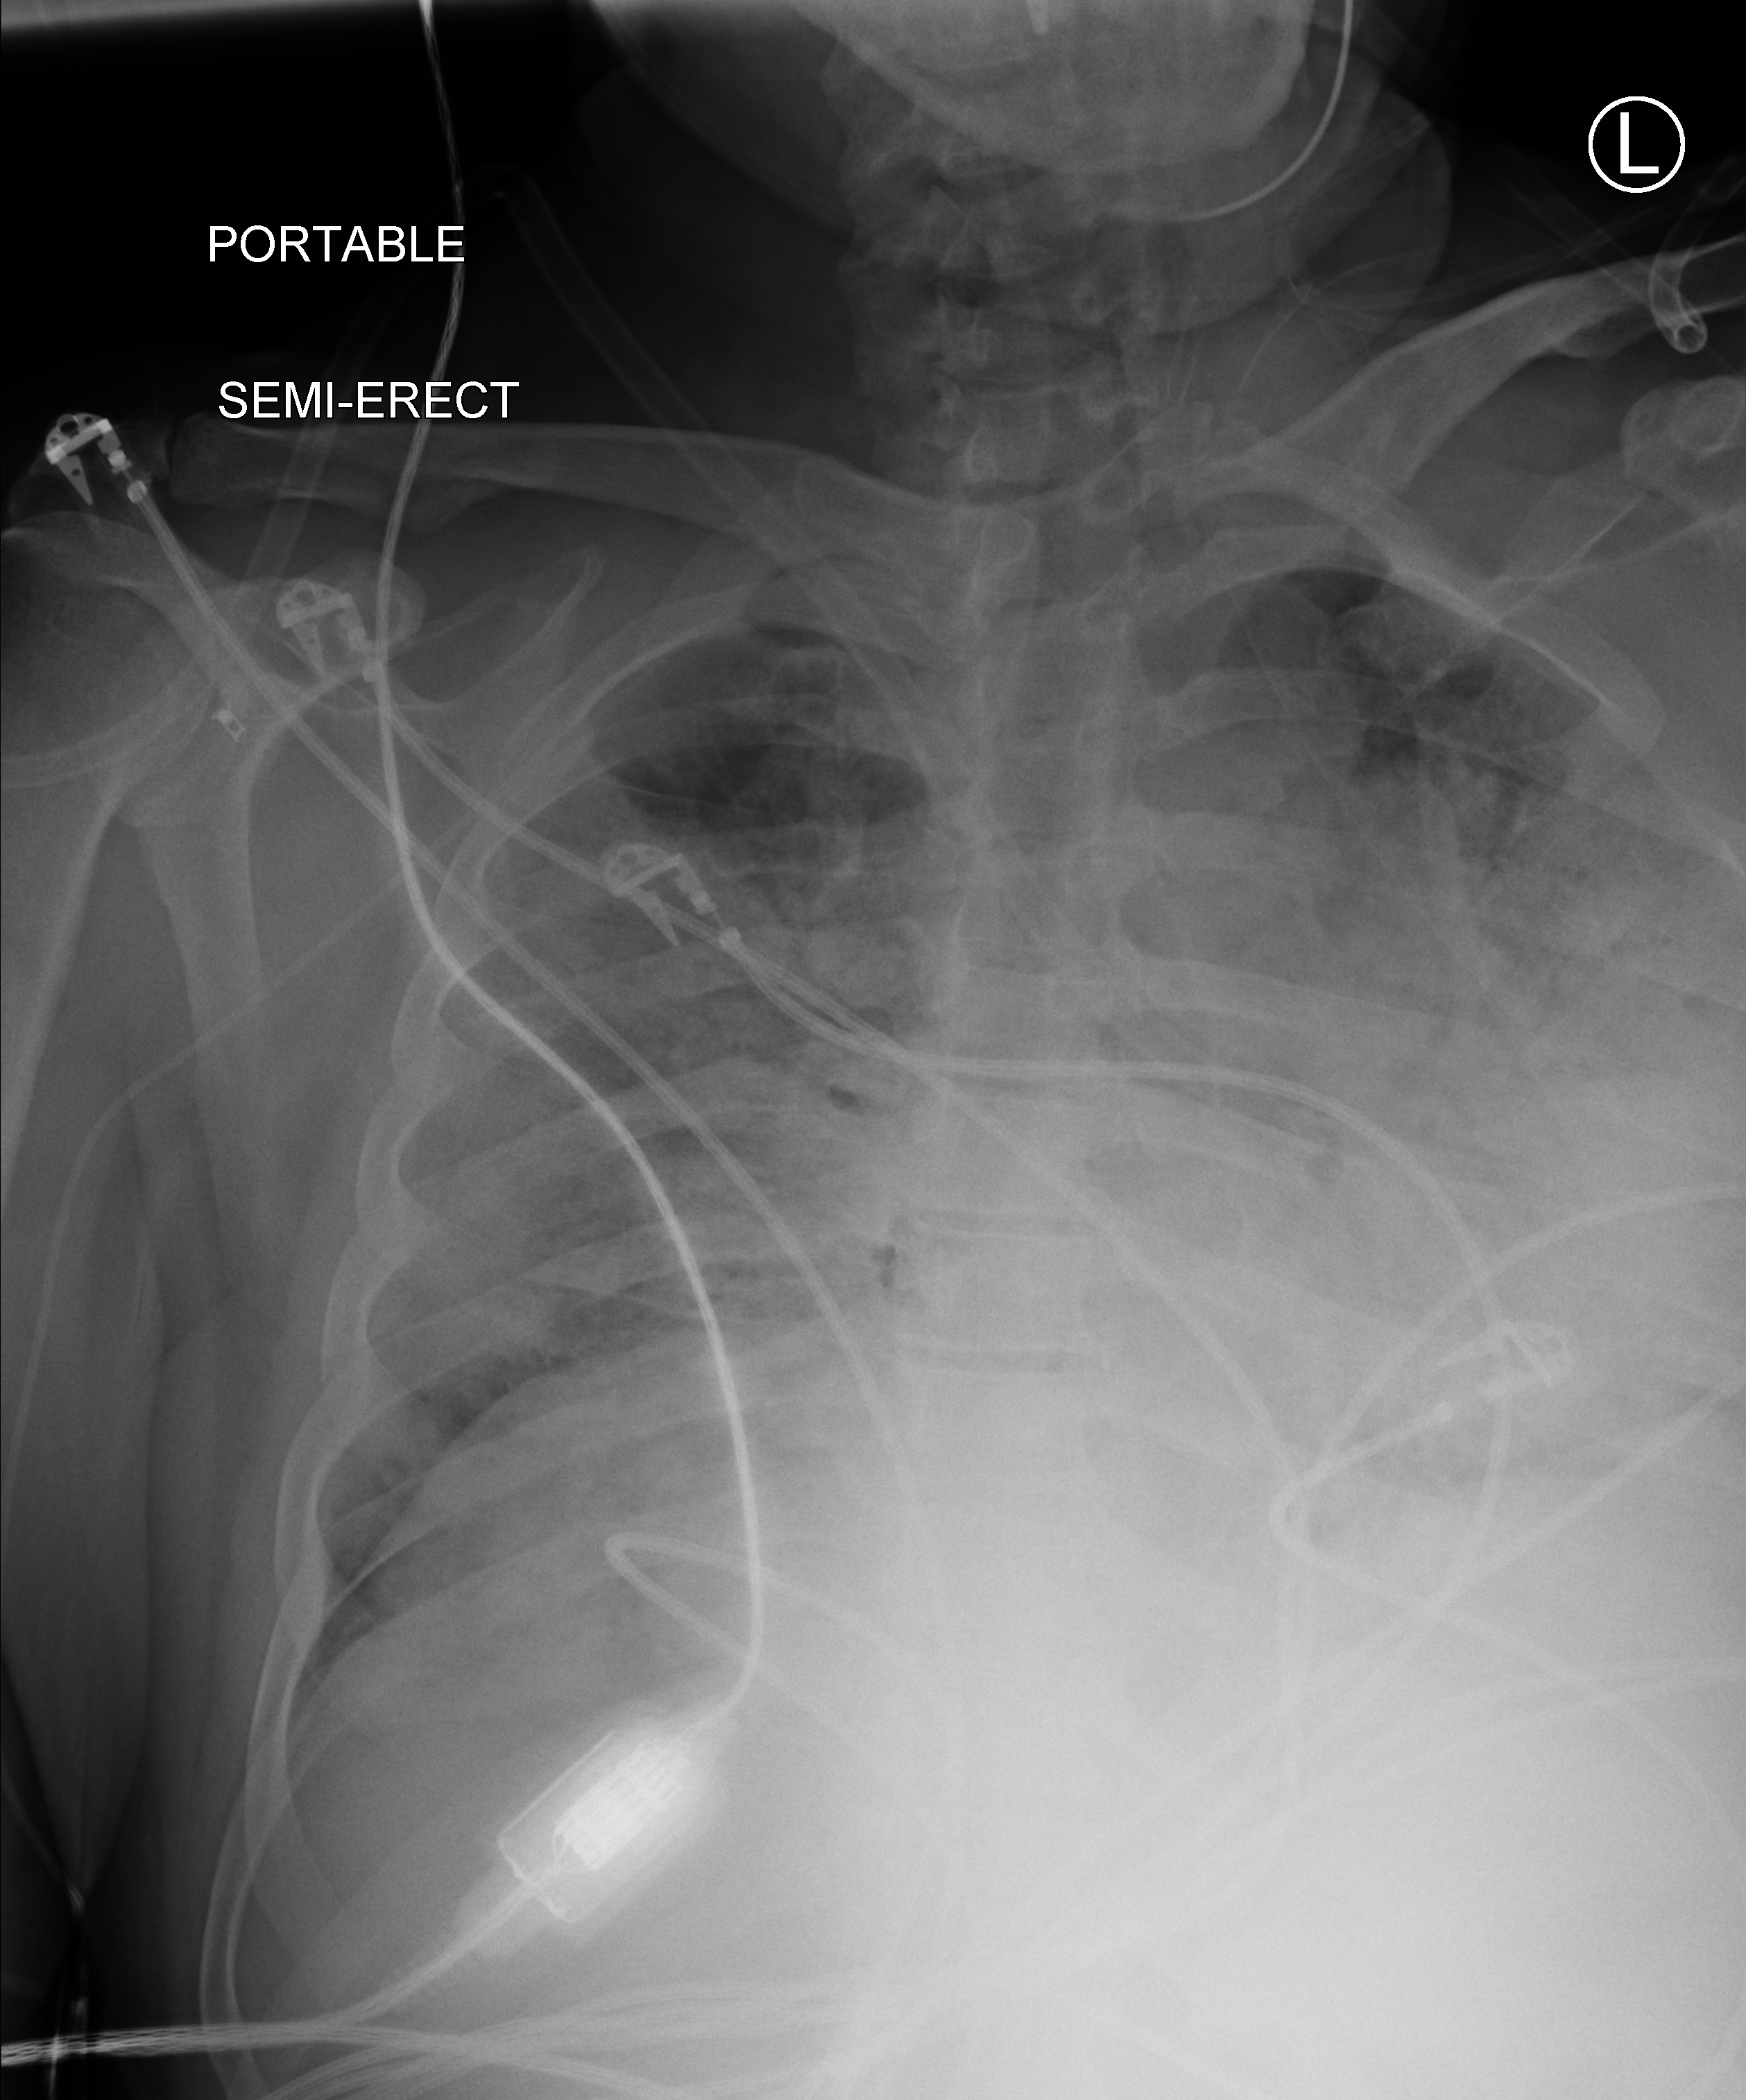
Portable chest radiograph; anteroposterior (AP) projection. Male patient hospitalised with COVID-19, age 18–59 years.
Hospital-stay facts (about this admission, not read from this image; timing relative to this image not recorded):
- admitted to intensive care during this hospital stay: yes
- other chronic lung disease (admission record): no